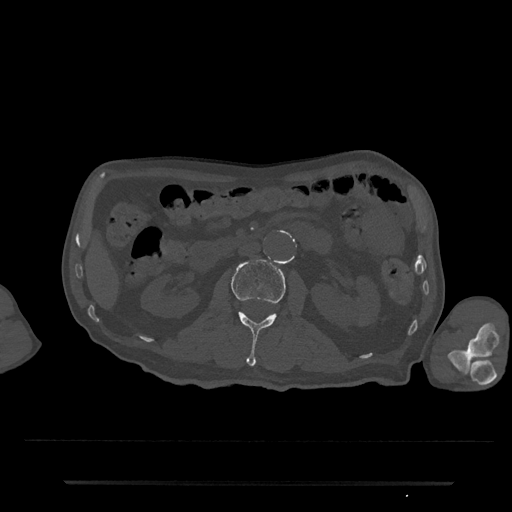
CT including the spine, one axial slice; slice 52 of 797 in the series (ordered by position); 120 kVp; bone window (W 1800 / L 400 HU); 0.5 mm slice thickness; 512 × 512 image matrix, field of view 427 × 427 mm. Patient: male, 74 years. From the clinical record (not read from this slice): primary cancer: prostate.
Annotated regions visible in this slice (semi-automatic segmentation, software-assisted and operator-edited):
- L2 vertebra: bounding box [x1, y1, x2, y2] px = [231, 259, 286, 367]